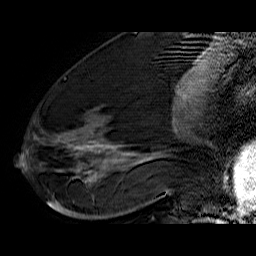
Breast MRI (dynamic contrast-enhanced), one sagittal slice. Slice 27 of 60 in the series (ordered by position). Dynamic contrast-enhanced series, time point 2 of 6 at this slice position (early post-contrast). 1.5 T. TE 6.4 ms, TR 32.9 ms. 256 × 256 image matrix. Female patient. From the clinical record (not read from this slice): setting: breast cancer imaged before/during neoadjuvant chemotherapy; receptor status: HR-positive, HER2-negative.
Annotated regions visible in this slice (semi-automatic segmentation, software-assisted and operator-edited):
- analysis volume of interest (the breast-tissue region the enhancement analysis was run in; not a lesion): bounding box <40,74,176,210> (left, top, right, bottom; pixels)
- tumour enhancement mask (voxels above the 100 % enhancement threshold inside the analysis volume of interest): <55,139,164,203>